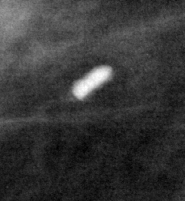
Cropped region of a digitized screen-film mammogram centred on a radiologist-marked abnormality; right breast; MLO view.
Finding: calcifications, morphology large rodlike, distribution segmental; BI-RADS assessment category 2; benign without callback (not worked up further).